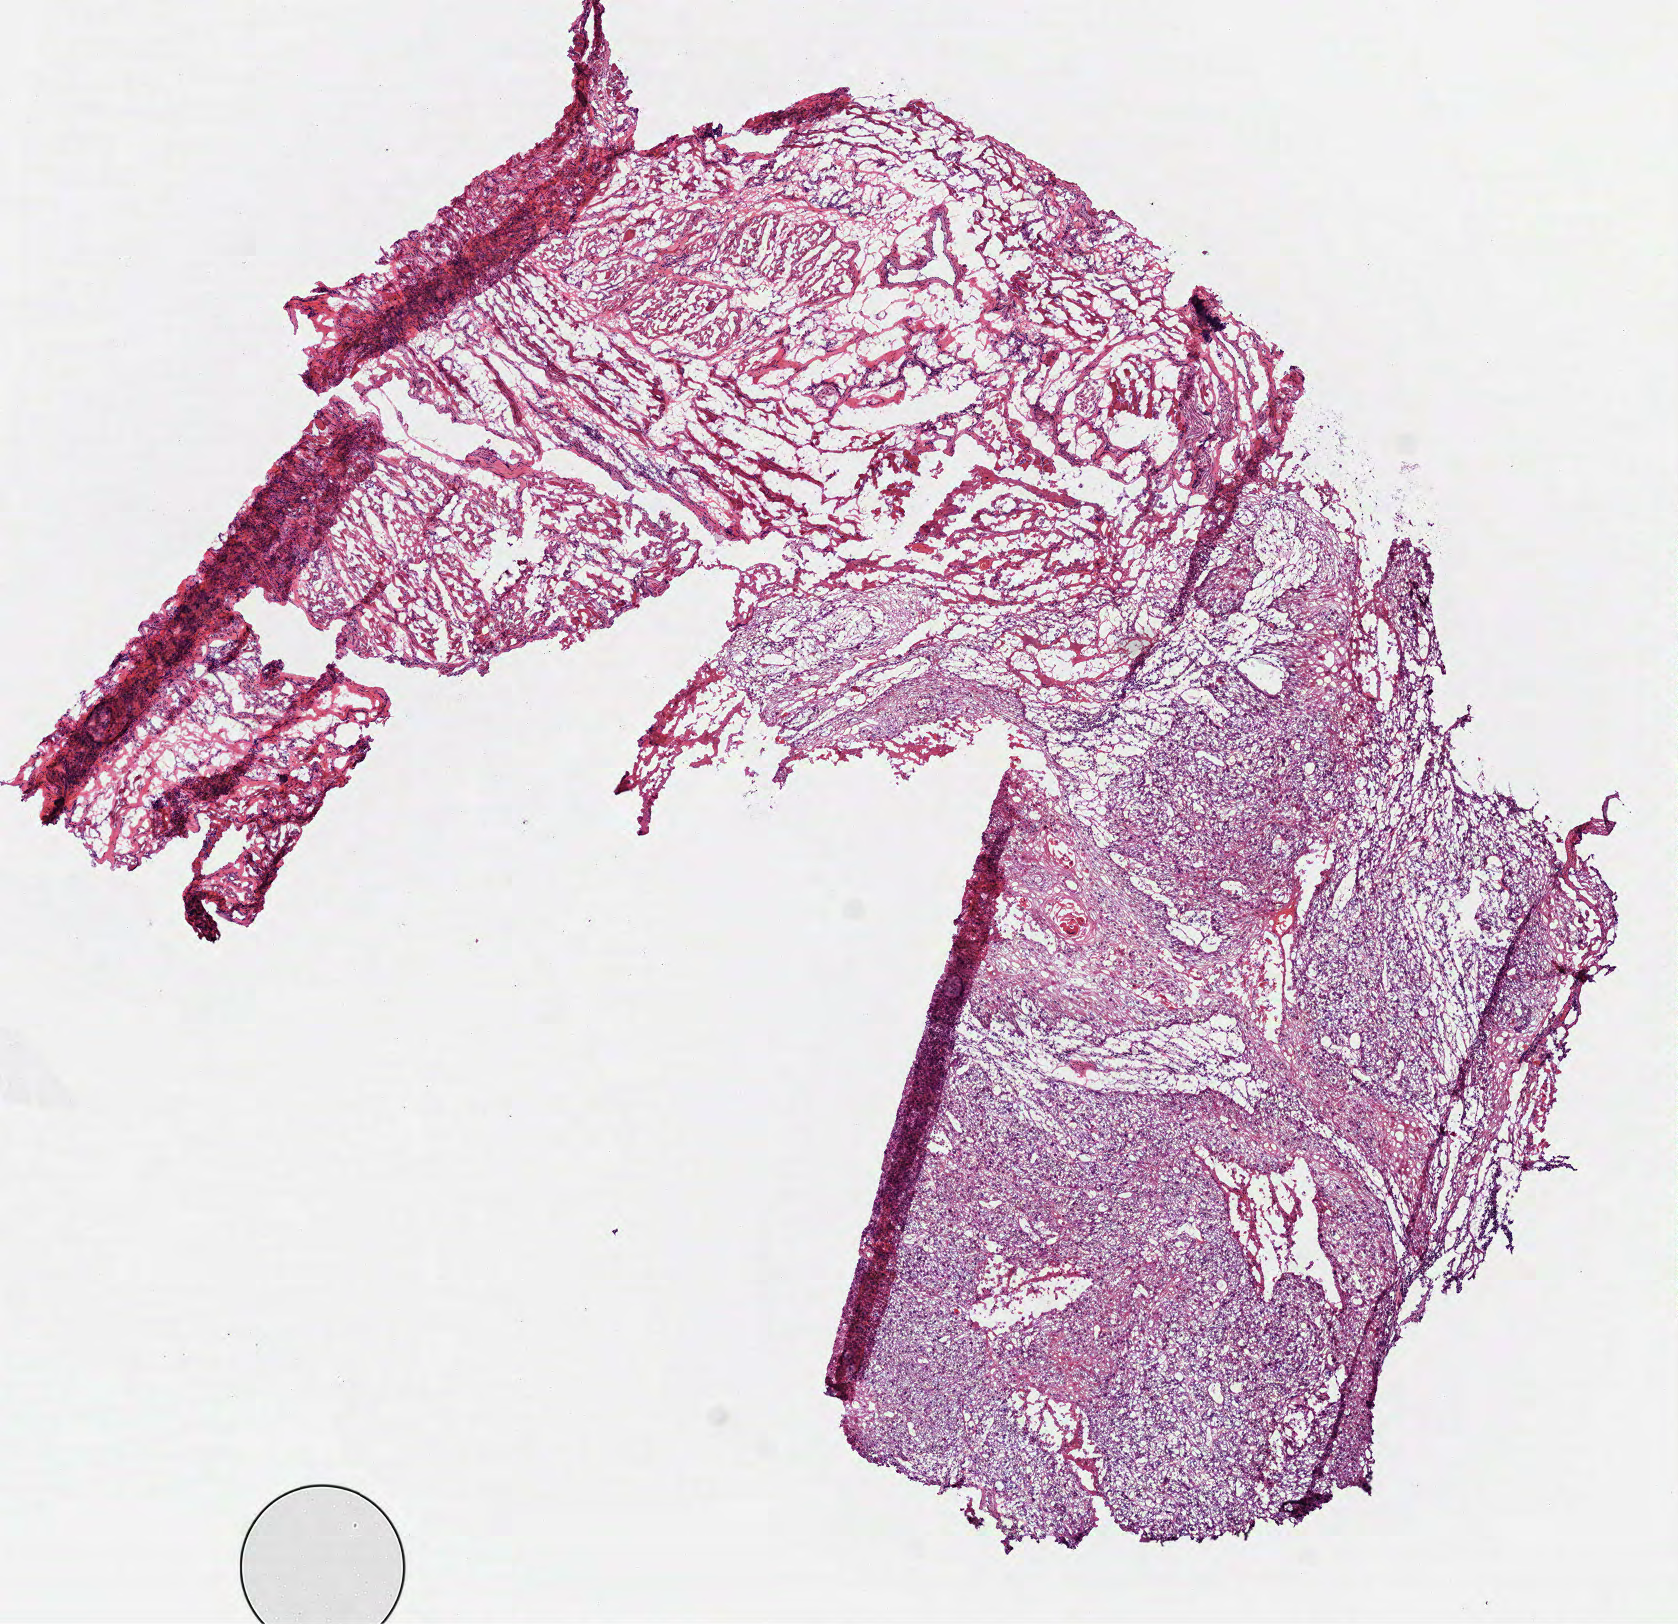
Digitized H&E tissue section (whole slide) — shown as a low-resolution overview of the whole scanned area (about 6.8 x 6.6 mm), frozen section, sample: primary tumour, head and neck. Male patient; age at initial diagnosis 48 years. Histologic grade: G2 (moderately differentiated). Composition of this section per pathologist review: tumour cells 50%, tumour nuclei 61%, normal cells 50%, stromal cells 0%, necrosis 0%. Inflammatory infiltration, as recorded: lymphocyte infiltration 5%, monocyte infiltration 0%, neutrophil infiltration 2%.
* histologic diagnosis: Squamous cell carcinoma, NOS (tongue, NOS)
* AJCC pathologic stage: III